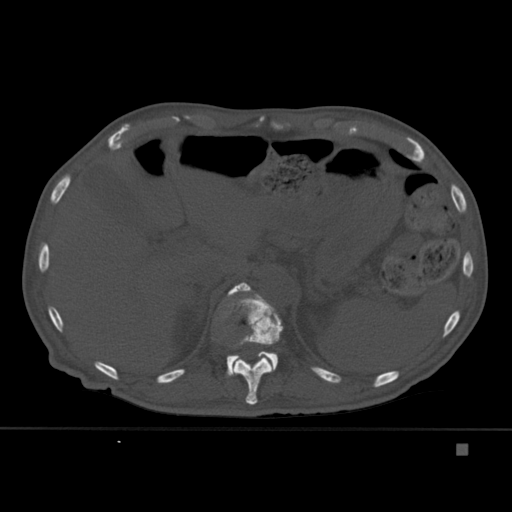
CT including the spine, one axial slice; position 212 of 451 along the scan axis; bone window (W 1800 / L 400 HU); 1.5 mm slice thickness; 512 × 512 image matrix, field of view 378 × 378 mm. Patient: male, 75 years. From the clinical record (not read from this slice): primary cancer: prostate.
Structures marked on this image (semi-automatic segmentation, software-assisted and operator-edited):
- T11 vertebra: bounding box (x1, y1, x2, y2) in pixels: (222, 291, 283, 405)
- T12 vertebra: (224, 282, 278, 377)